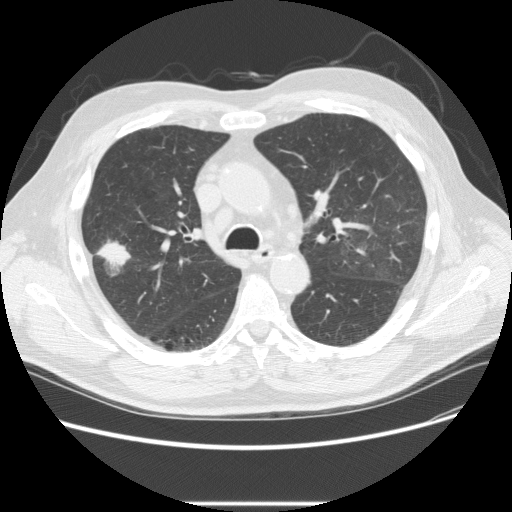
Low-dose screening chest CT, one axial slice. Slice 153 of 233 in the series (ordered by position). Reconstruction kernel STANDARD. Lung window (W 1500 / L -600 HU). 512 × 512 image matrix.
Structures marked on this image (outlined manually by an expert reader):
- lesion 2 (tumor, upper lobe of right lung): bounding box (x1, y1, x2, y2) in pixels: (96, 240, 130, 275)